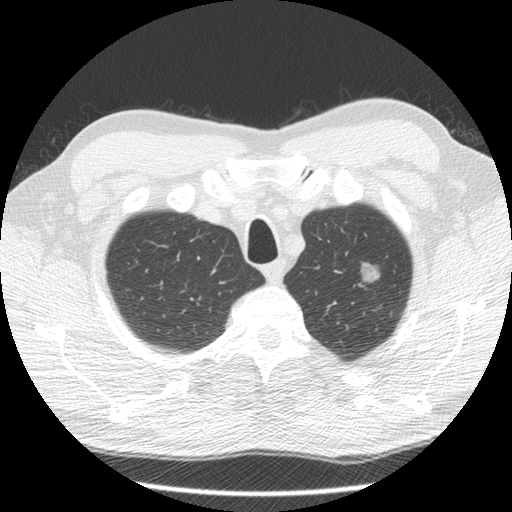
Low-dose screening chest CT, one axial slice. Position 117 of 132 along the scan axis. 120 kVp. Lung window (W 1500 / L -600 HU). 512 × 512 image matrix, field of view 340 × 340 mm.
Outlined on this slice (expert manual segmentation):
- lesion 1 (tumor, upper lobe of left lung): bounding box [x1, y1, x2, y2] px = [360, 262, 380, 283]